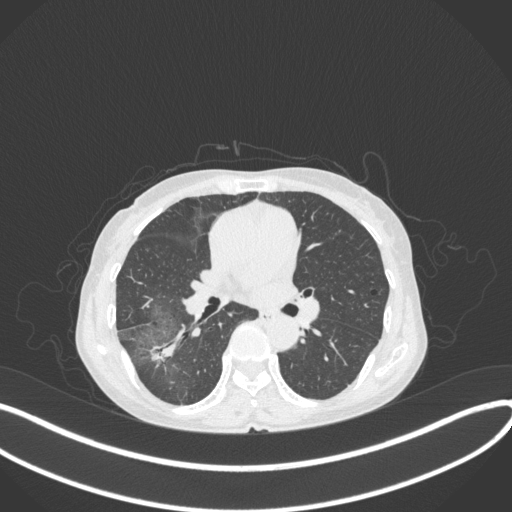
Chest CT, one axial slice; slice 214 of 379 in the series (ordered by position); 120 kVp; lung window (W 1500 / L -600 HU); 1 mm slice thickness; 512 × 512 image matrix, field of view 400 × 400 mm. Female patient, age 69 years. From the clinical record (not read from this slice): clinical TNM (as recorded): T1b N0 M0; histopathological grade: G2-3.
Outlined on this slice (bounding box drawn by a radiologist):
- lung tumour (recorded histology: adenocarcinoma): bounding box [x1, y1, x2, y2] px = [148, 331, 182, 365]